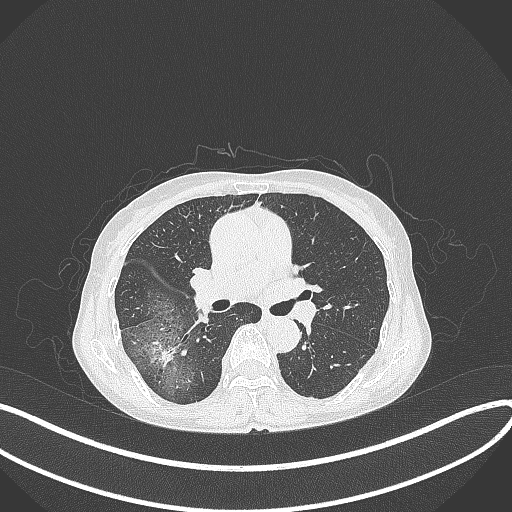
Chest CT, one axial slice; position 228 of 371 along the scan axis; 120 kVp; lung window (W 1500 / L -600 HU); 512 × 512 image matrix, field of view 400 × 400 mm. Patient: female, 69 years. From the clinical record (not read from this slice): clinical TNM (as recorded): T1b N0 M0.
Outlined on this slice (bounding box drawn by a radiologist):
- lung tumour (recorded histology: adenocarcinoma): bounding box (x1, y1, x2, y2) in pixels: (144, 334, 178, 370)